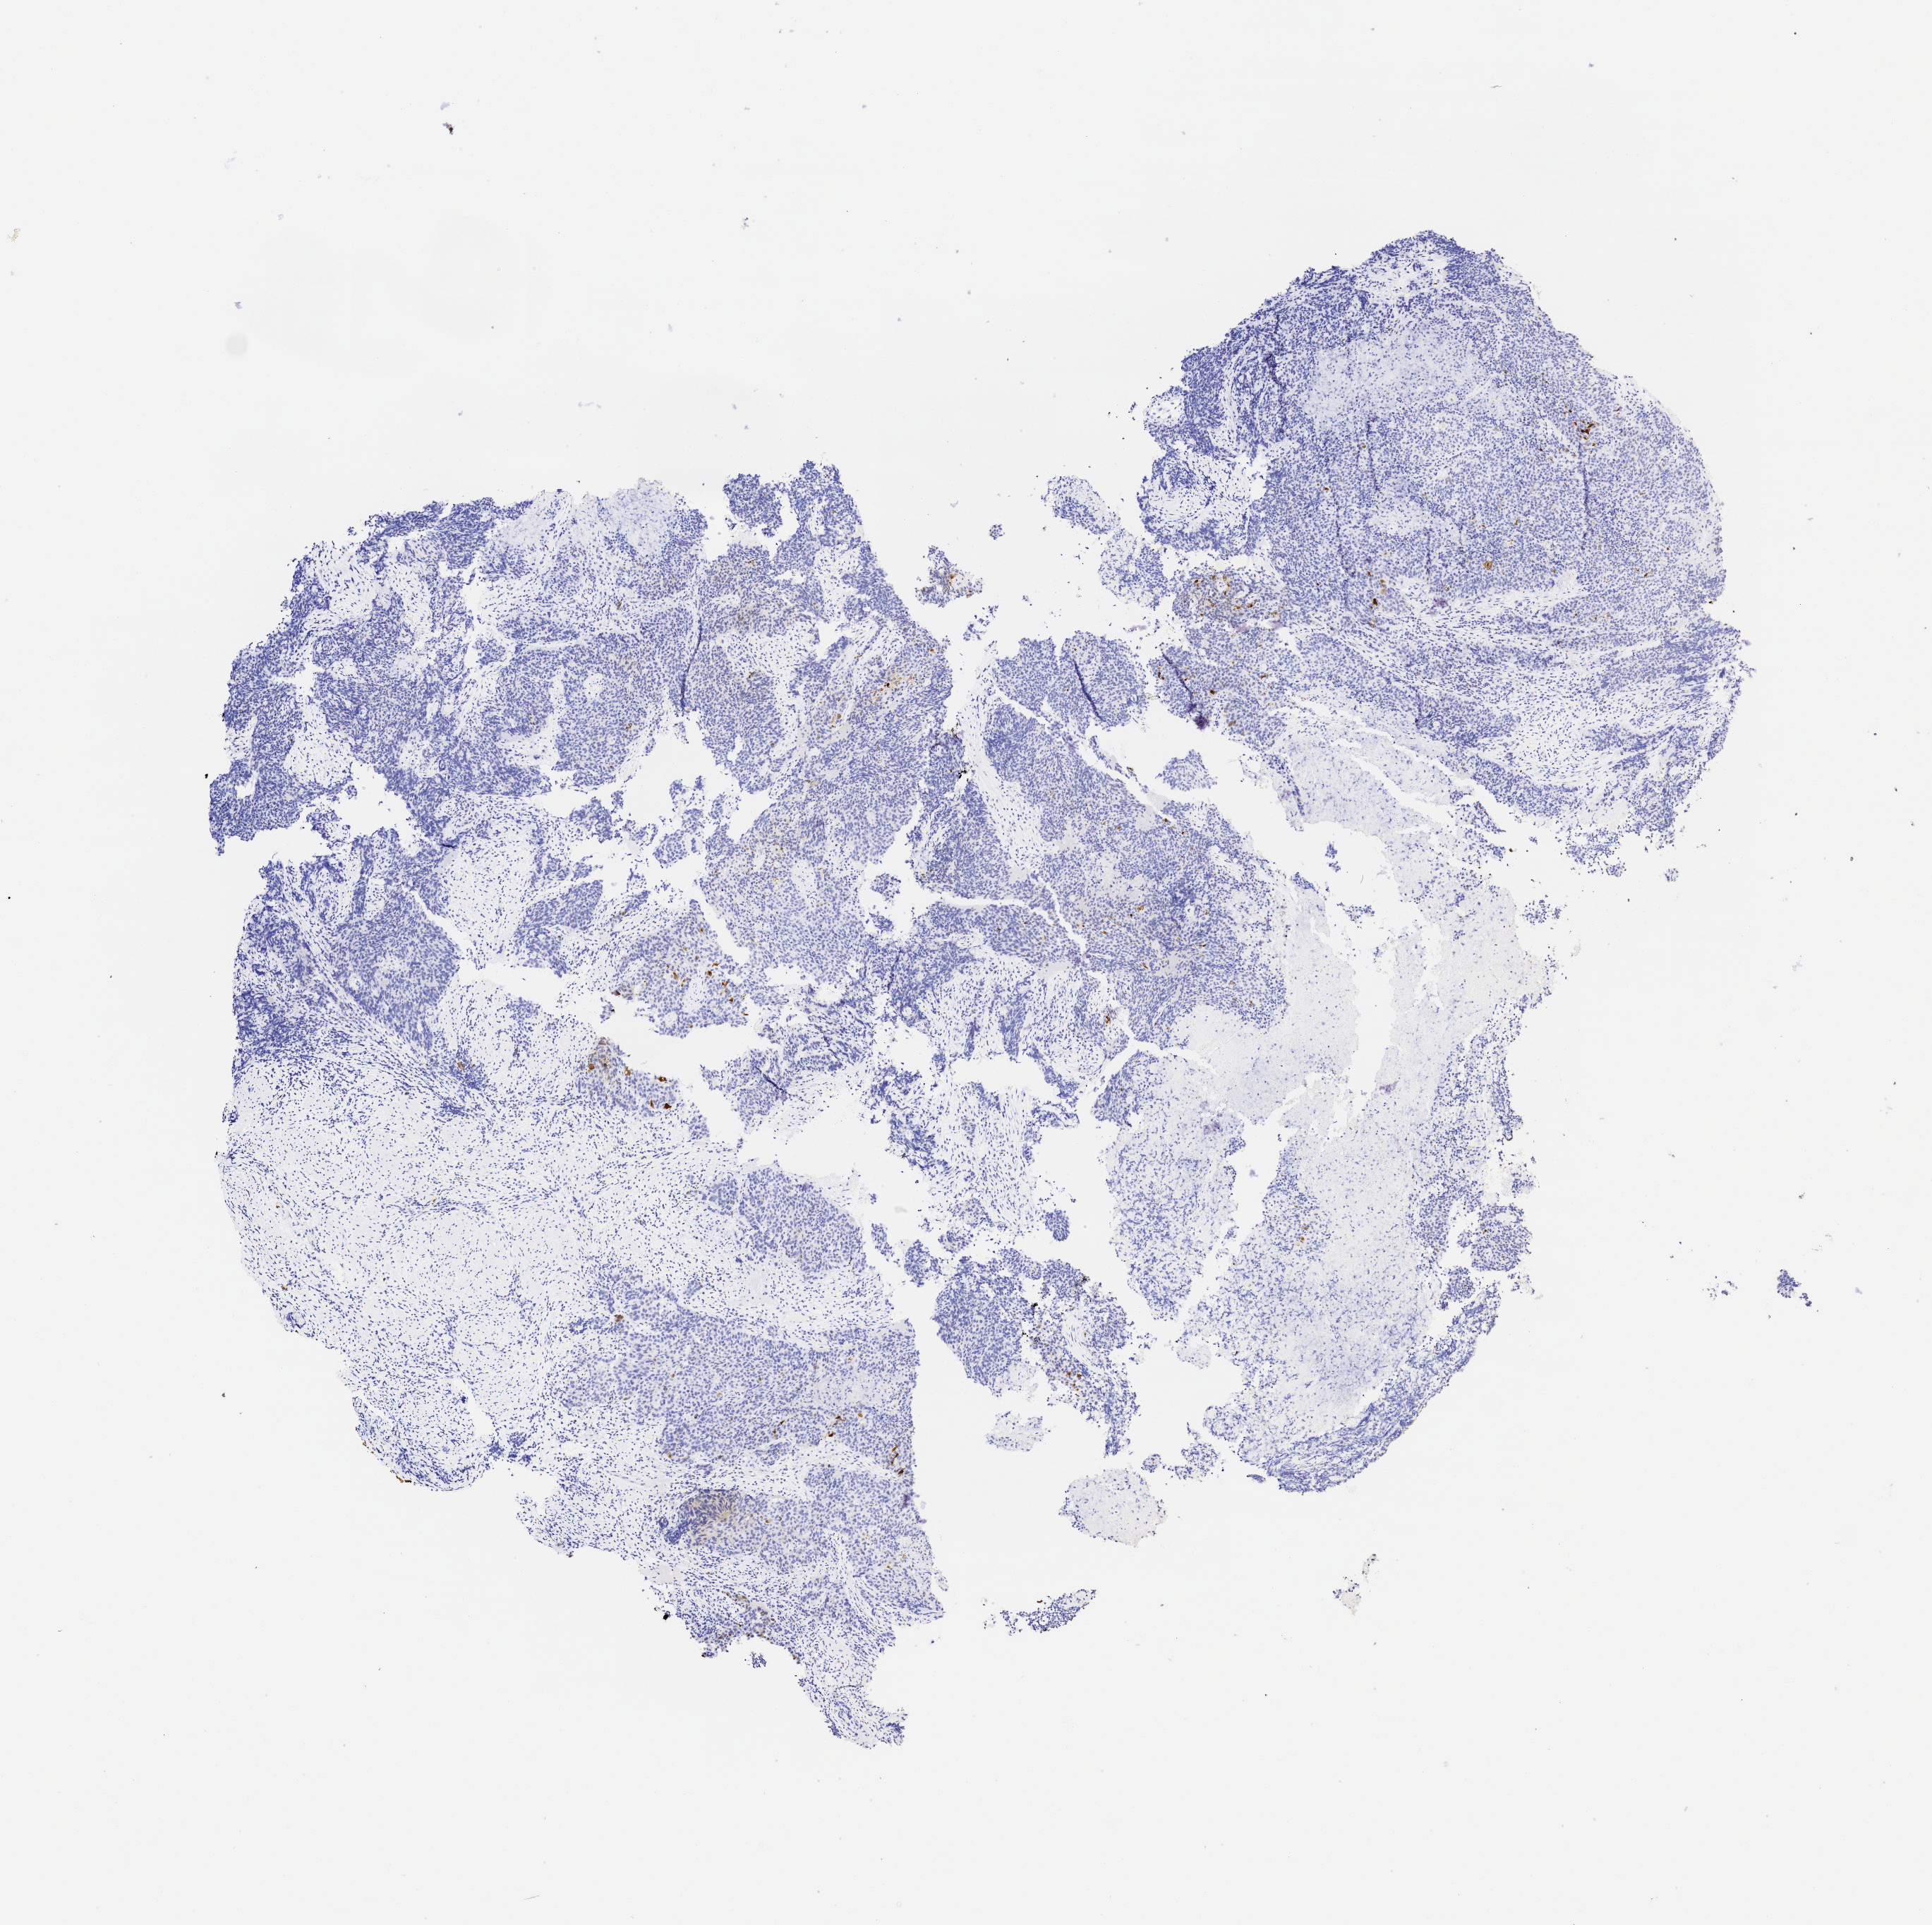
Whole-slide image, immunohistochemical stain for p16 (p16INK4a), a low-resolution overview of the entire scanned area, about 5.5 x 5.5 mm; specimen: tumor tissue; anatomic site: cervix. Patient female; 54 years old.
Diagnosis: Squamous cell carcinoma, large cell, nonkeratinizing, NOS.